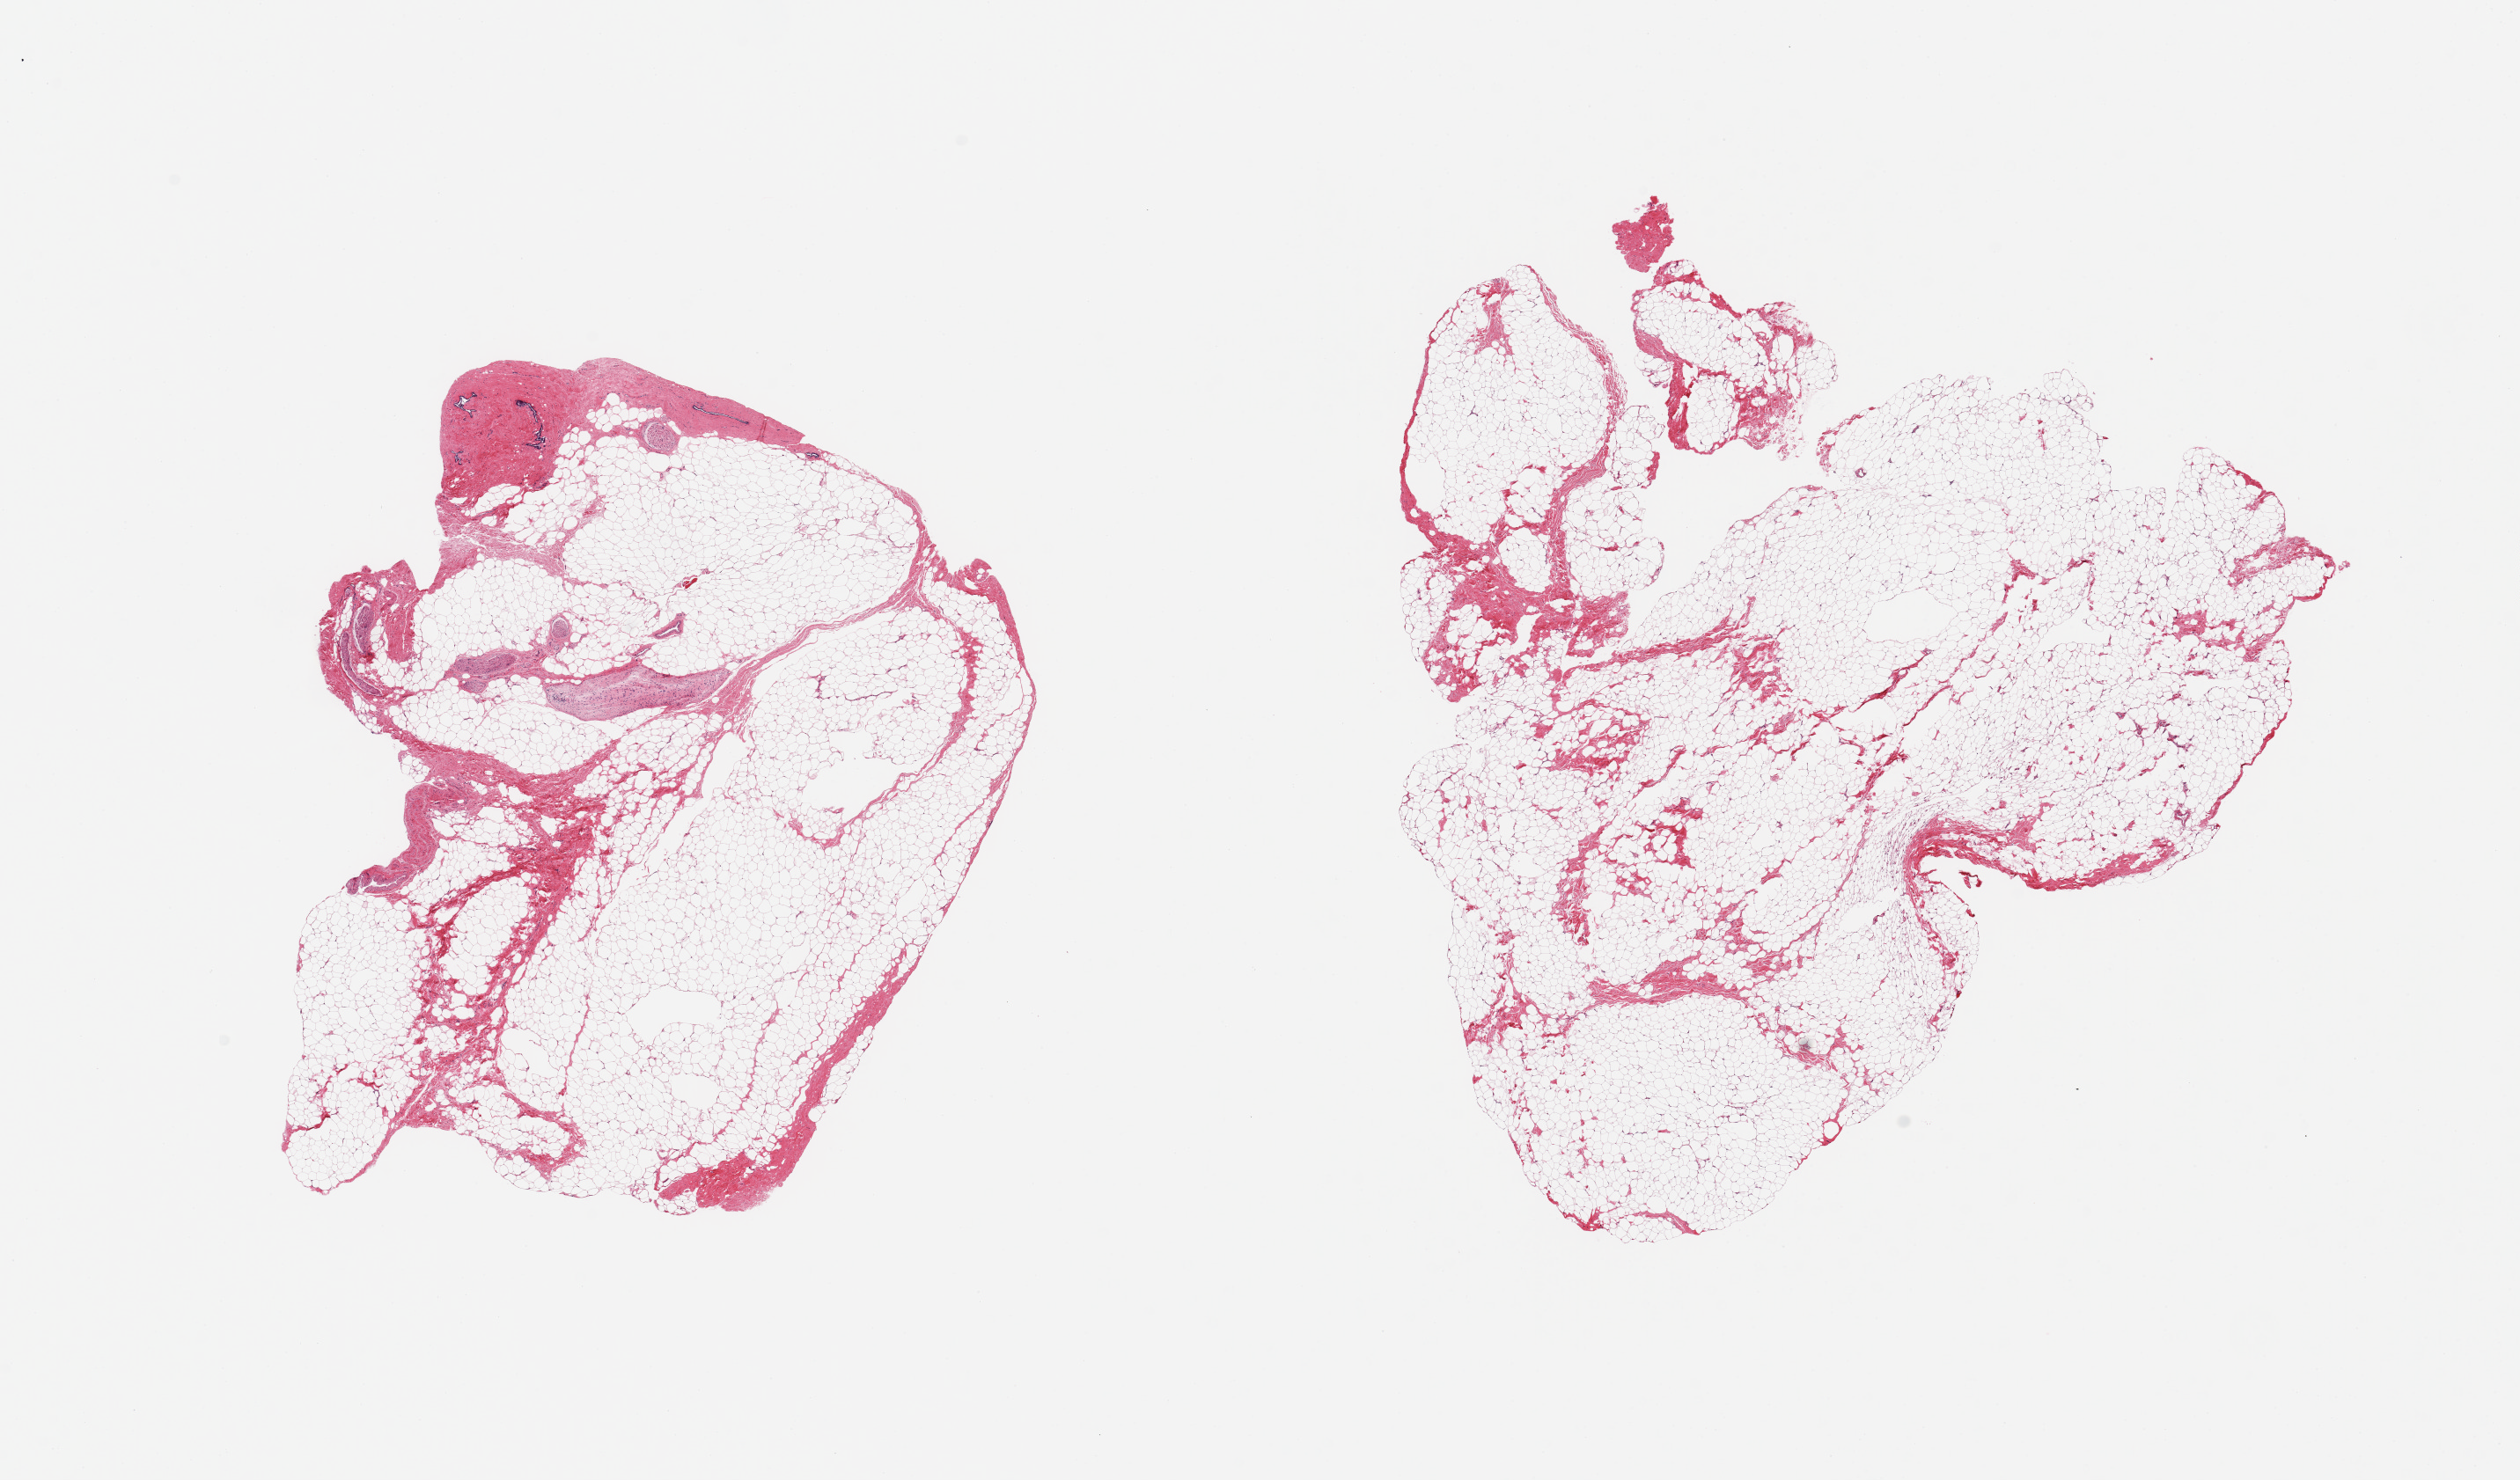
Whole-slide image, hematoxylin and eosin (H&E) stain, brightfield, shown as a low-resolution overview of the whole scanned area (about 22.6 x 13.3 mm). PAXgene-fixed paraffin-embedded (PFPE) section. Target tissue: breast. Donor tissue sample. Male donor.
Reviewer comment on this tissue sample: 2 pieces mainly fibroadipose tissue; trace ductal elements.